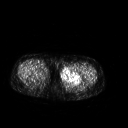
FDG PET of an extremity soft-tissue mass (from a PET/CT study), one axial slice; position 230 of 267 along the scan axis; 3.27 mm slice thickness; 128 × 128 image matrix. Female patient, age 42 years. From the clinical record (not read from this slice): histological type: pleiomorphic leiomyosarcoma; grade: intermediate; site of the primary tumour: left thigh.
Annotated regions visible in this slice (expert contour drawn on MRI and transferred to this co-registered scan by the dataset authors):
- gross tumour volume including surrounding oedema: bounding box (x1, y1, x2, y2) in pixels: (60, 67, 83, 83)
- gross tumour volume (mass): (60, 67, 81, 83)